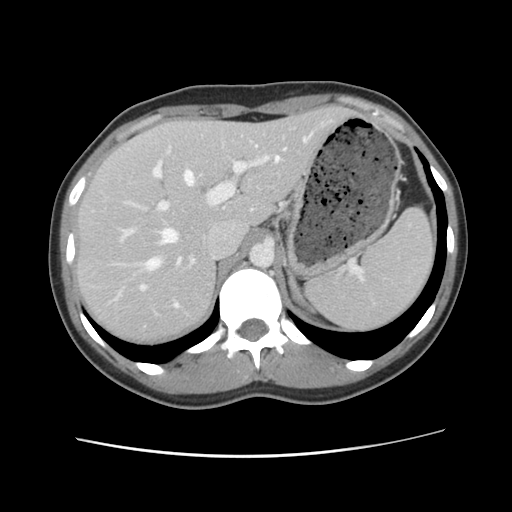
Contrast-enhanced abdominal CT, one axial slice; slice 79 of 134 in the series (ordered by position); 120 kVp; intravenous contrast given; soft-tissue window (W 400 / L 40 HU); 2.5 mm slice thickness; 512 × 512 image matrix. Female patient, age 33 years. From the clinical record (not read from this slice): diagnosis: colorectal cancer liver metastases, imaged before liver resection; multiple liver metastases: yes; largest metastasis: 4.5 cm; disease in both lobes: yes.
Outlined on this slice (outlined manually by an expert reader):
- hepatic veins: bounding box (x1, y1, x2, y2) in pixels: (147, 137, 308, 307)
- liver: (77, 108, 351, 345)
- planned liver remnant (the part of the liver to remain after resection): (78, 107, 352, 345)
- portal vein (with intrahepatic branches): (122, 139, 287, 289)